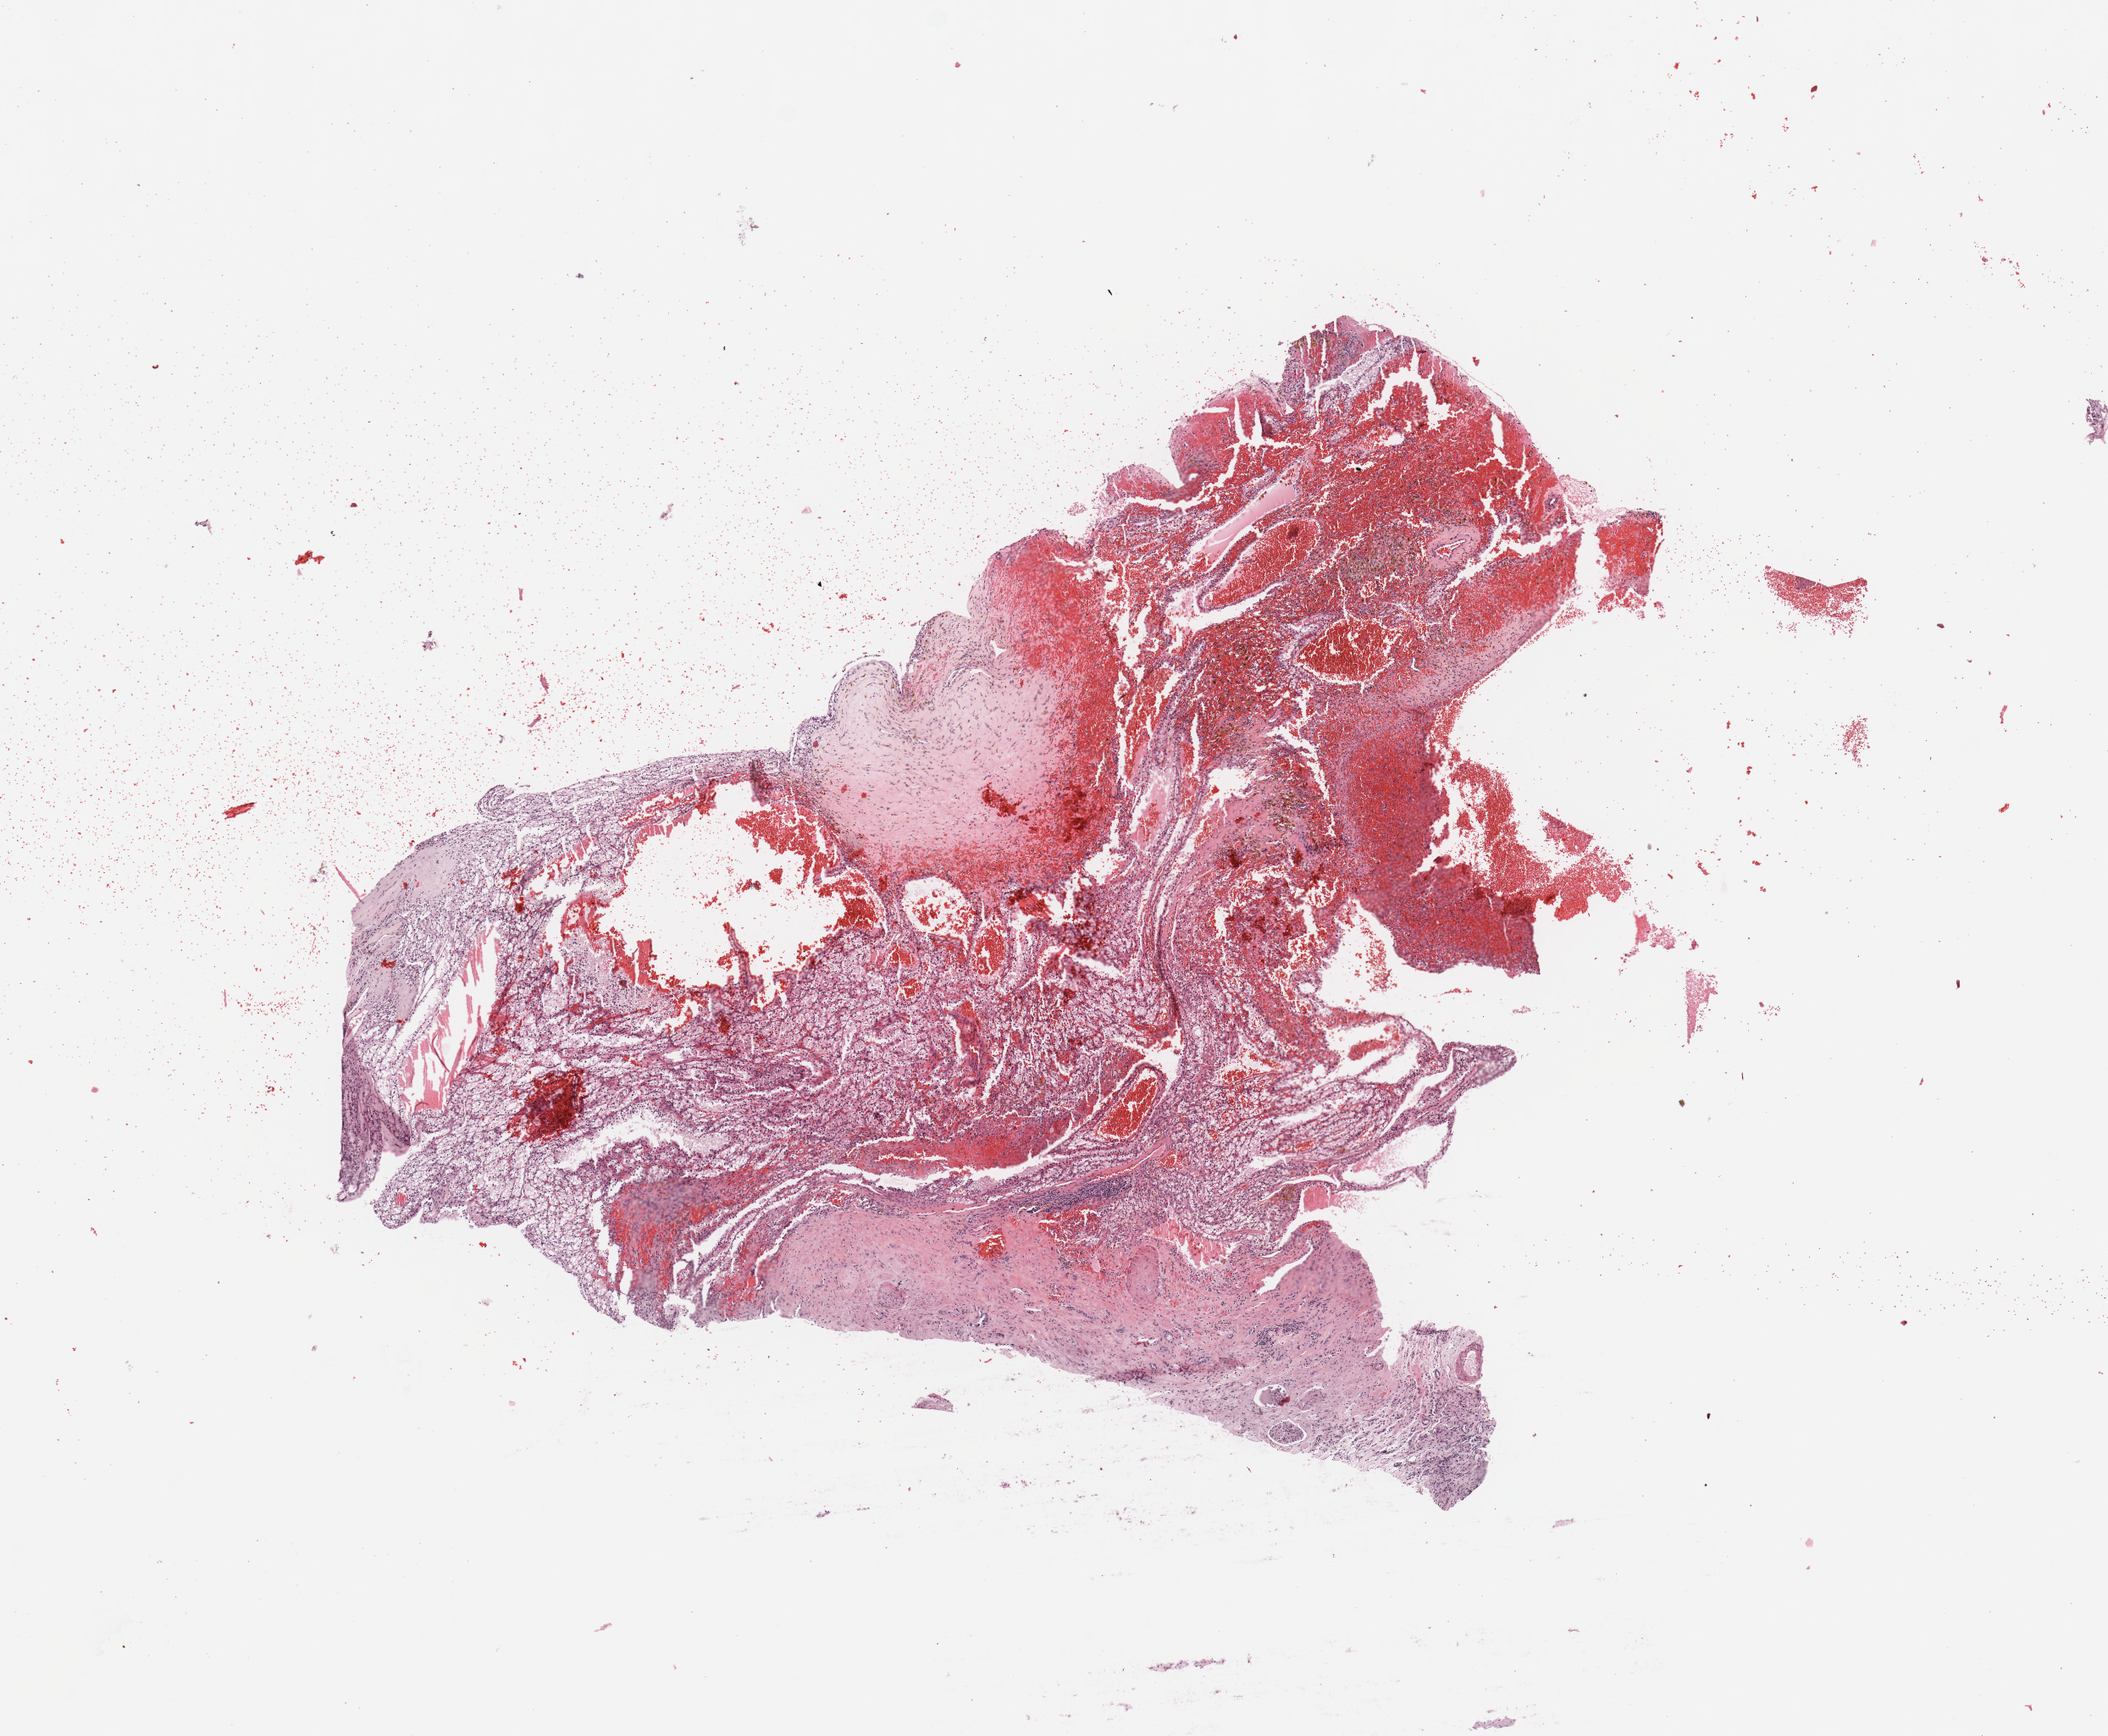
H&E whole-slide image, a low-resolution overview of the entire scanned area, about 9.8 x 8.1 mm (from a 20x scan). Tumour tissue sample, sampled site: kidney. Female, 78 y/o. Histologic grade: G2 (moderately differentiated). Slide review estimates, as recorded: tumour nuclei 80%, necrosis 5%.
* AJCC pathologic stage: I
* primary tumour site (as recorded): lower pole
* diagnosis: Renal cell carcinoma, NOS